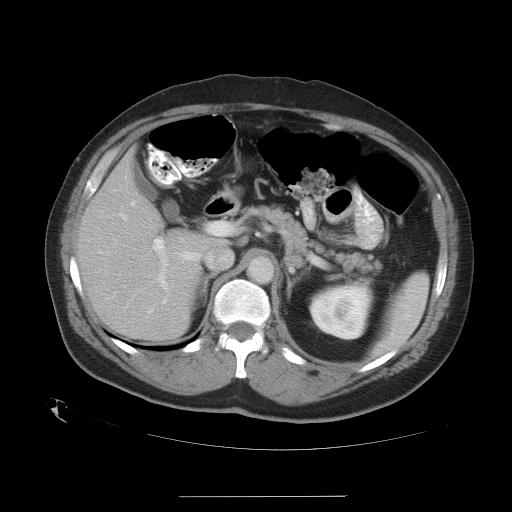
Contrast-enhanced abdominal CT, one axial slice; slice 19 of 35 in the series (ordered by position); reconstruction kernel STANDARD; 120 kVp; intravenous contrast given; soft-tissue window (W 400 / L 40 HU); 7.5 mm slice thickness; 512 × 512 image matrix. Male patient, age 67 years. From the clinical record (not read from this slice): diagnosis: colorectal cancer liver metastases, imaged before liver resection; multiple liver metastases: no; largest metastasis: 2.3 cm; chemotherapy before resection: no.
Outlined on this slice (manually delineated by an expert):
- hepatic veins: box from (x=114, y=201) to (x=152, y=313) px
- liver: (x=78, y=155)–(x=216, y=340)
- planned liver remnant (the part of the liver to remain after resection): (x=79, y=155)–(x=216, y=340)
- portal vein (with intrahepatic branches): (x=115, y=213)–(x=231, y=289)